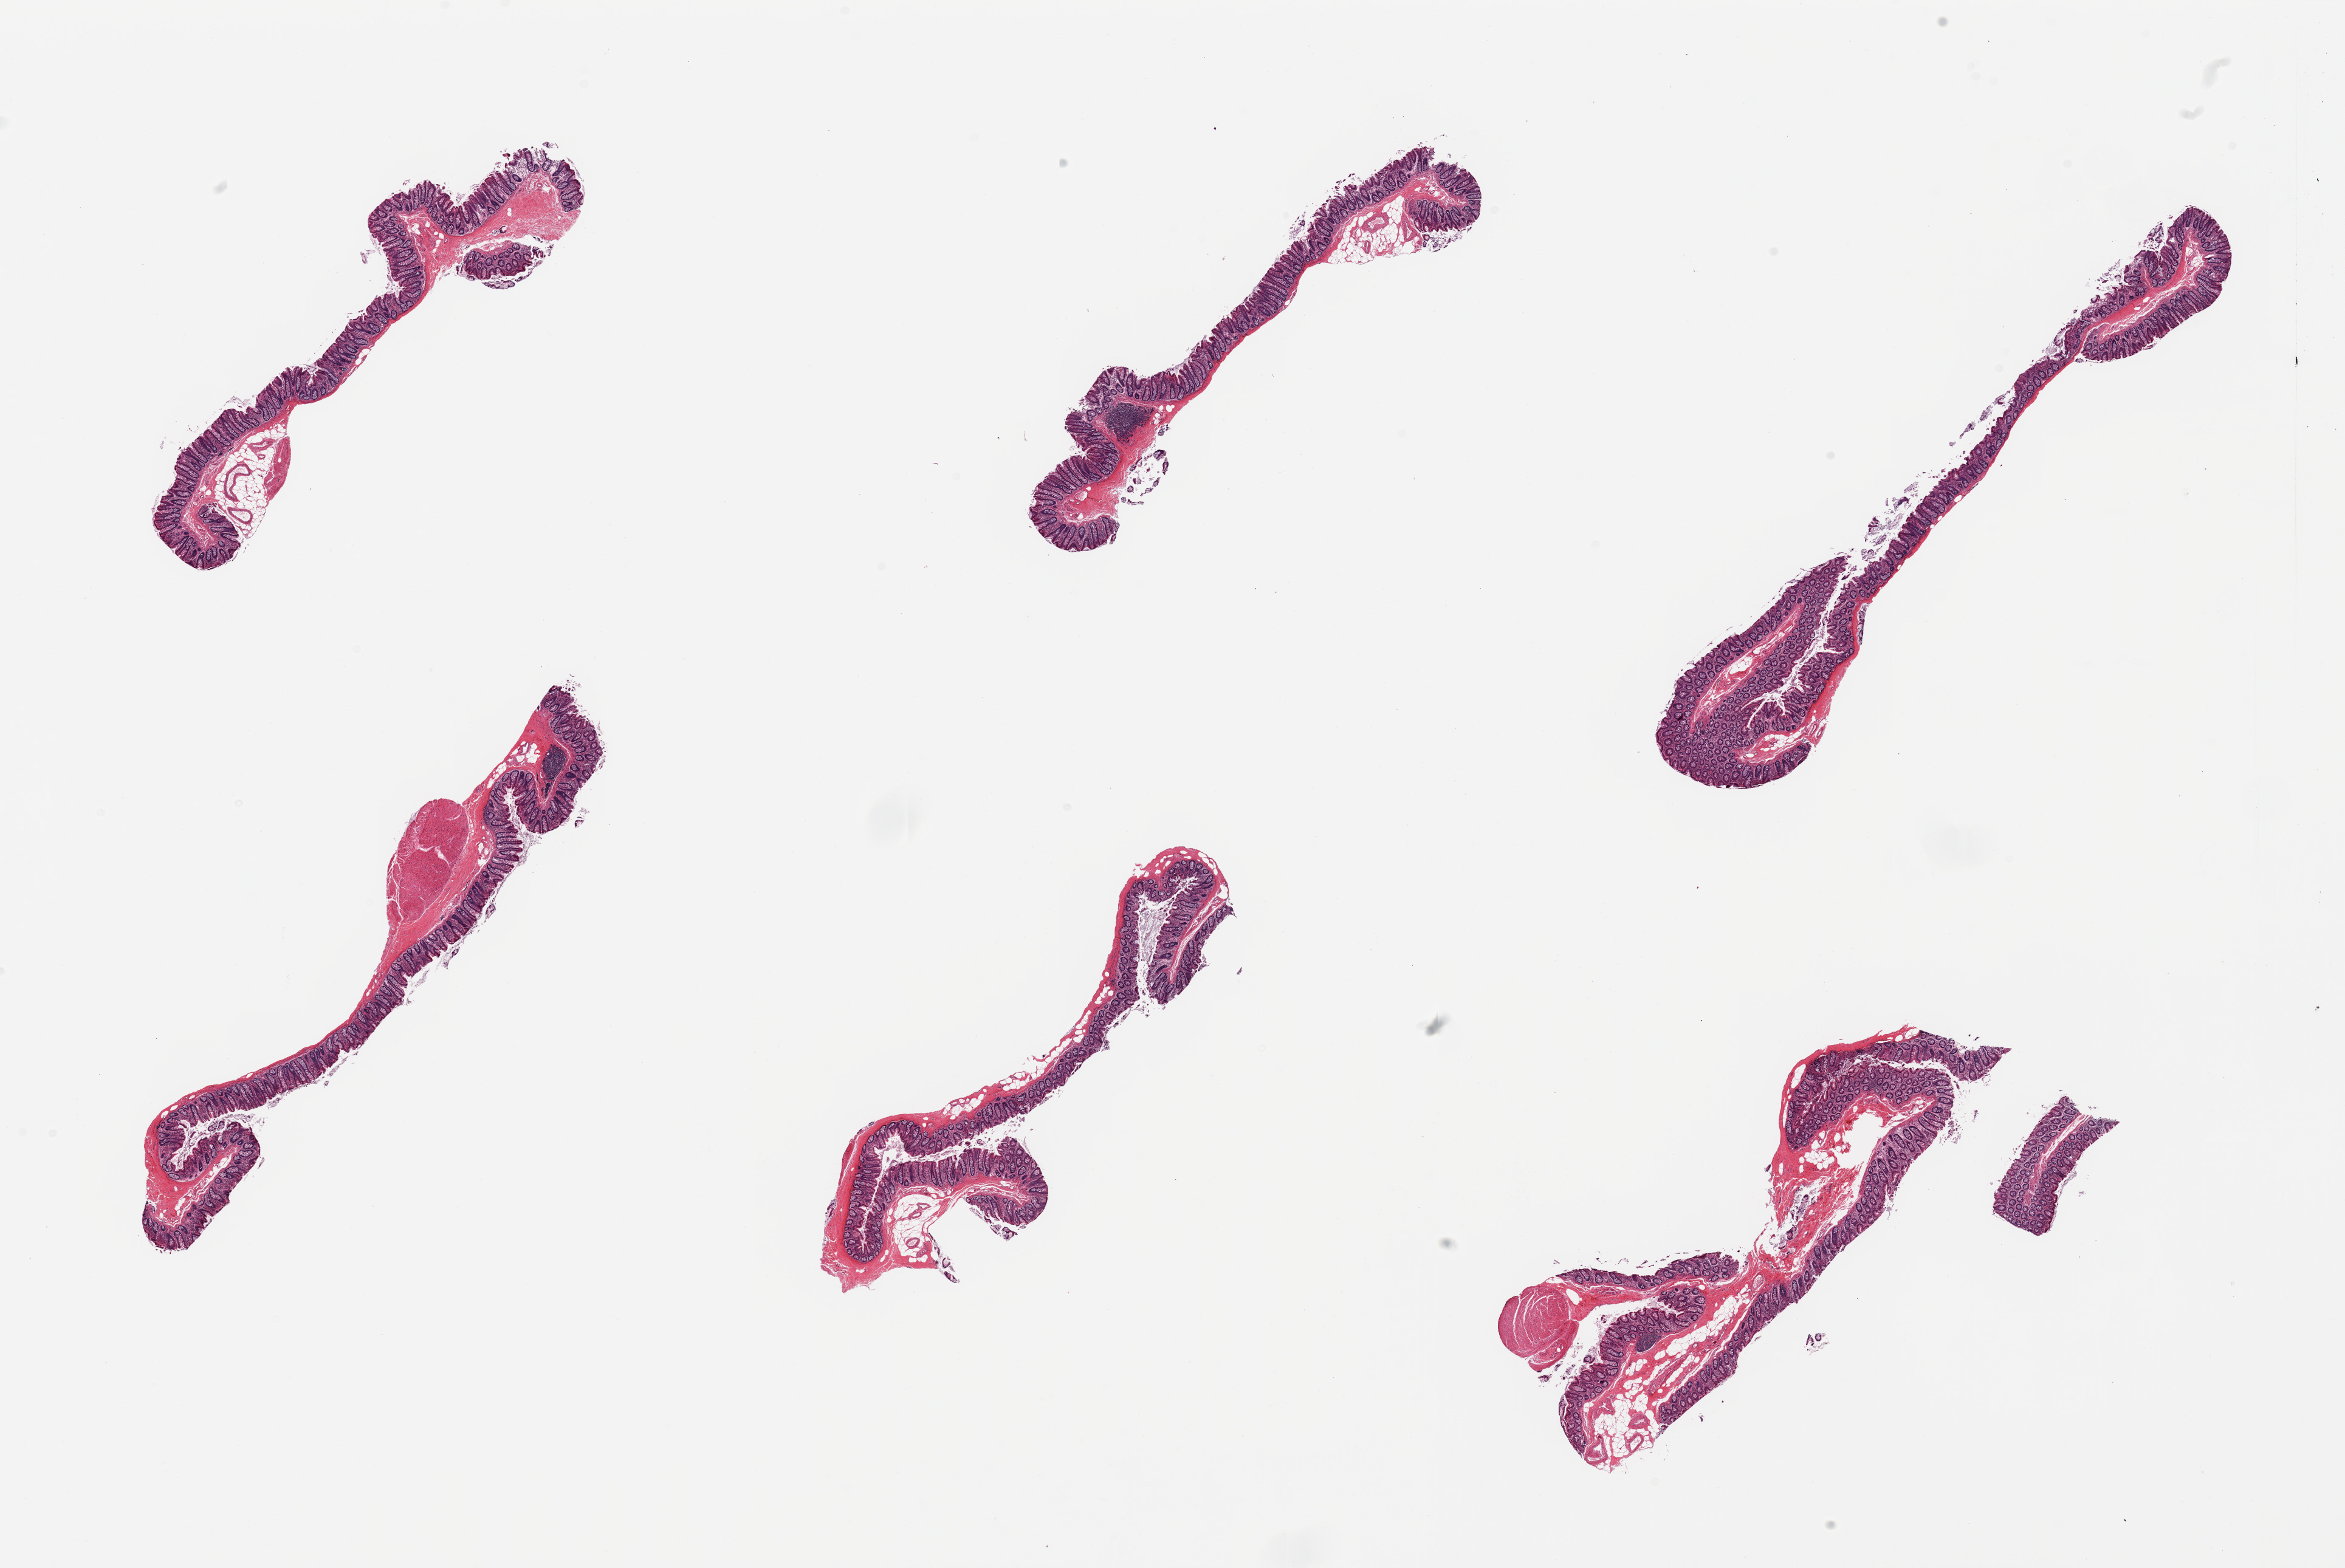
Whole-slide image, H&E stain, brightfield, shown as a low-resolution overview of the whole scanned area (about 30.5 x 20.4 mm, from a 20x scan). PAXgene-fixed, paraffin-embedded tissue. Target tissue: transverse colon. Tissue donor sample. Donor sex: male.
Pathologist's review note for this sample: 6 pieces; all contain only mucosa, no muscularis.